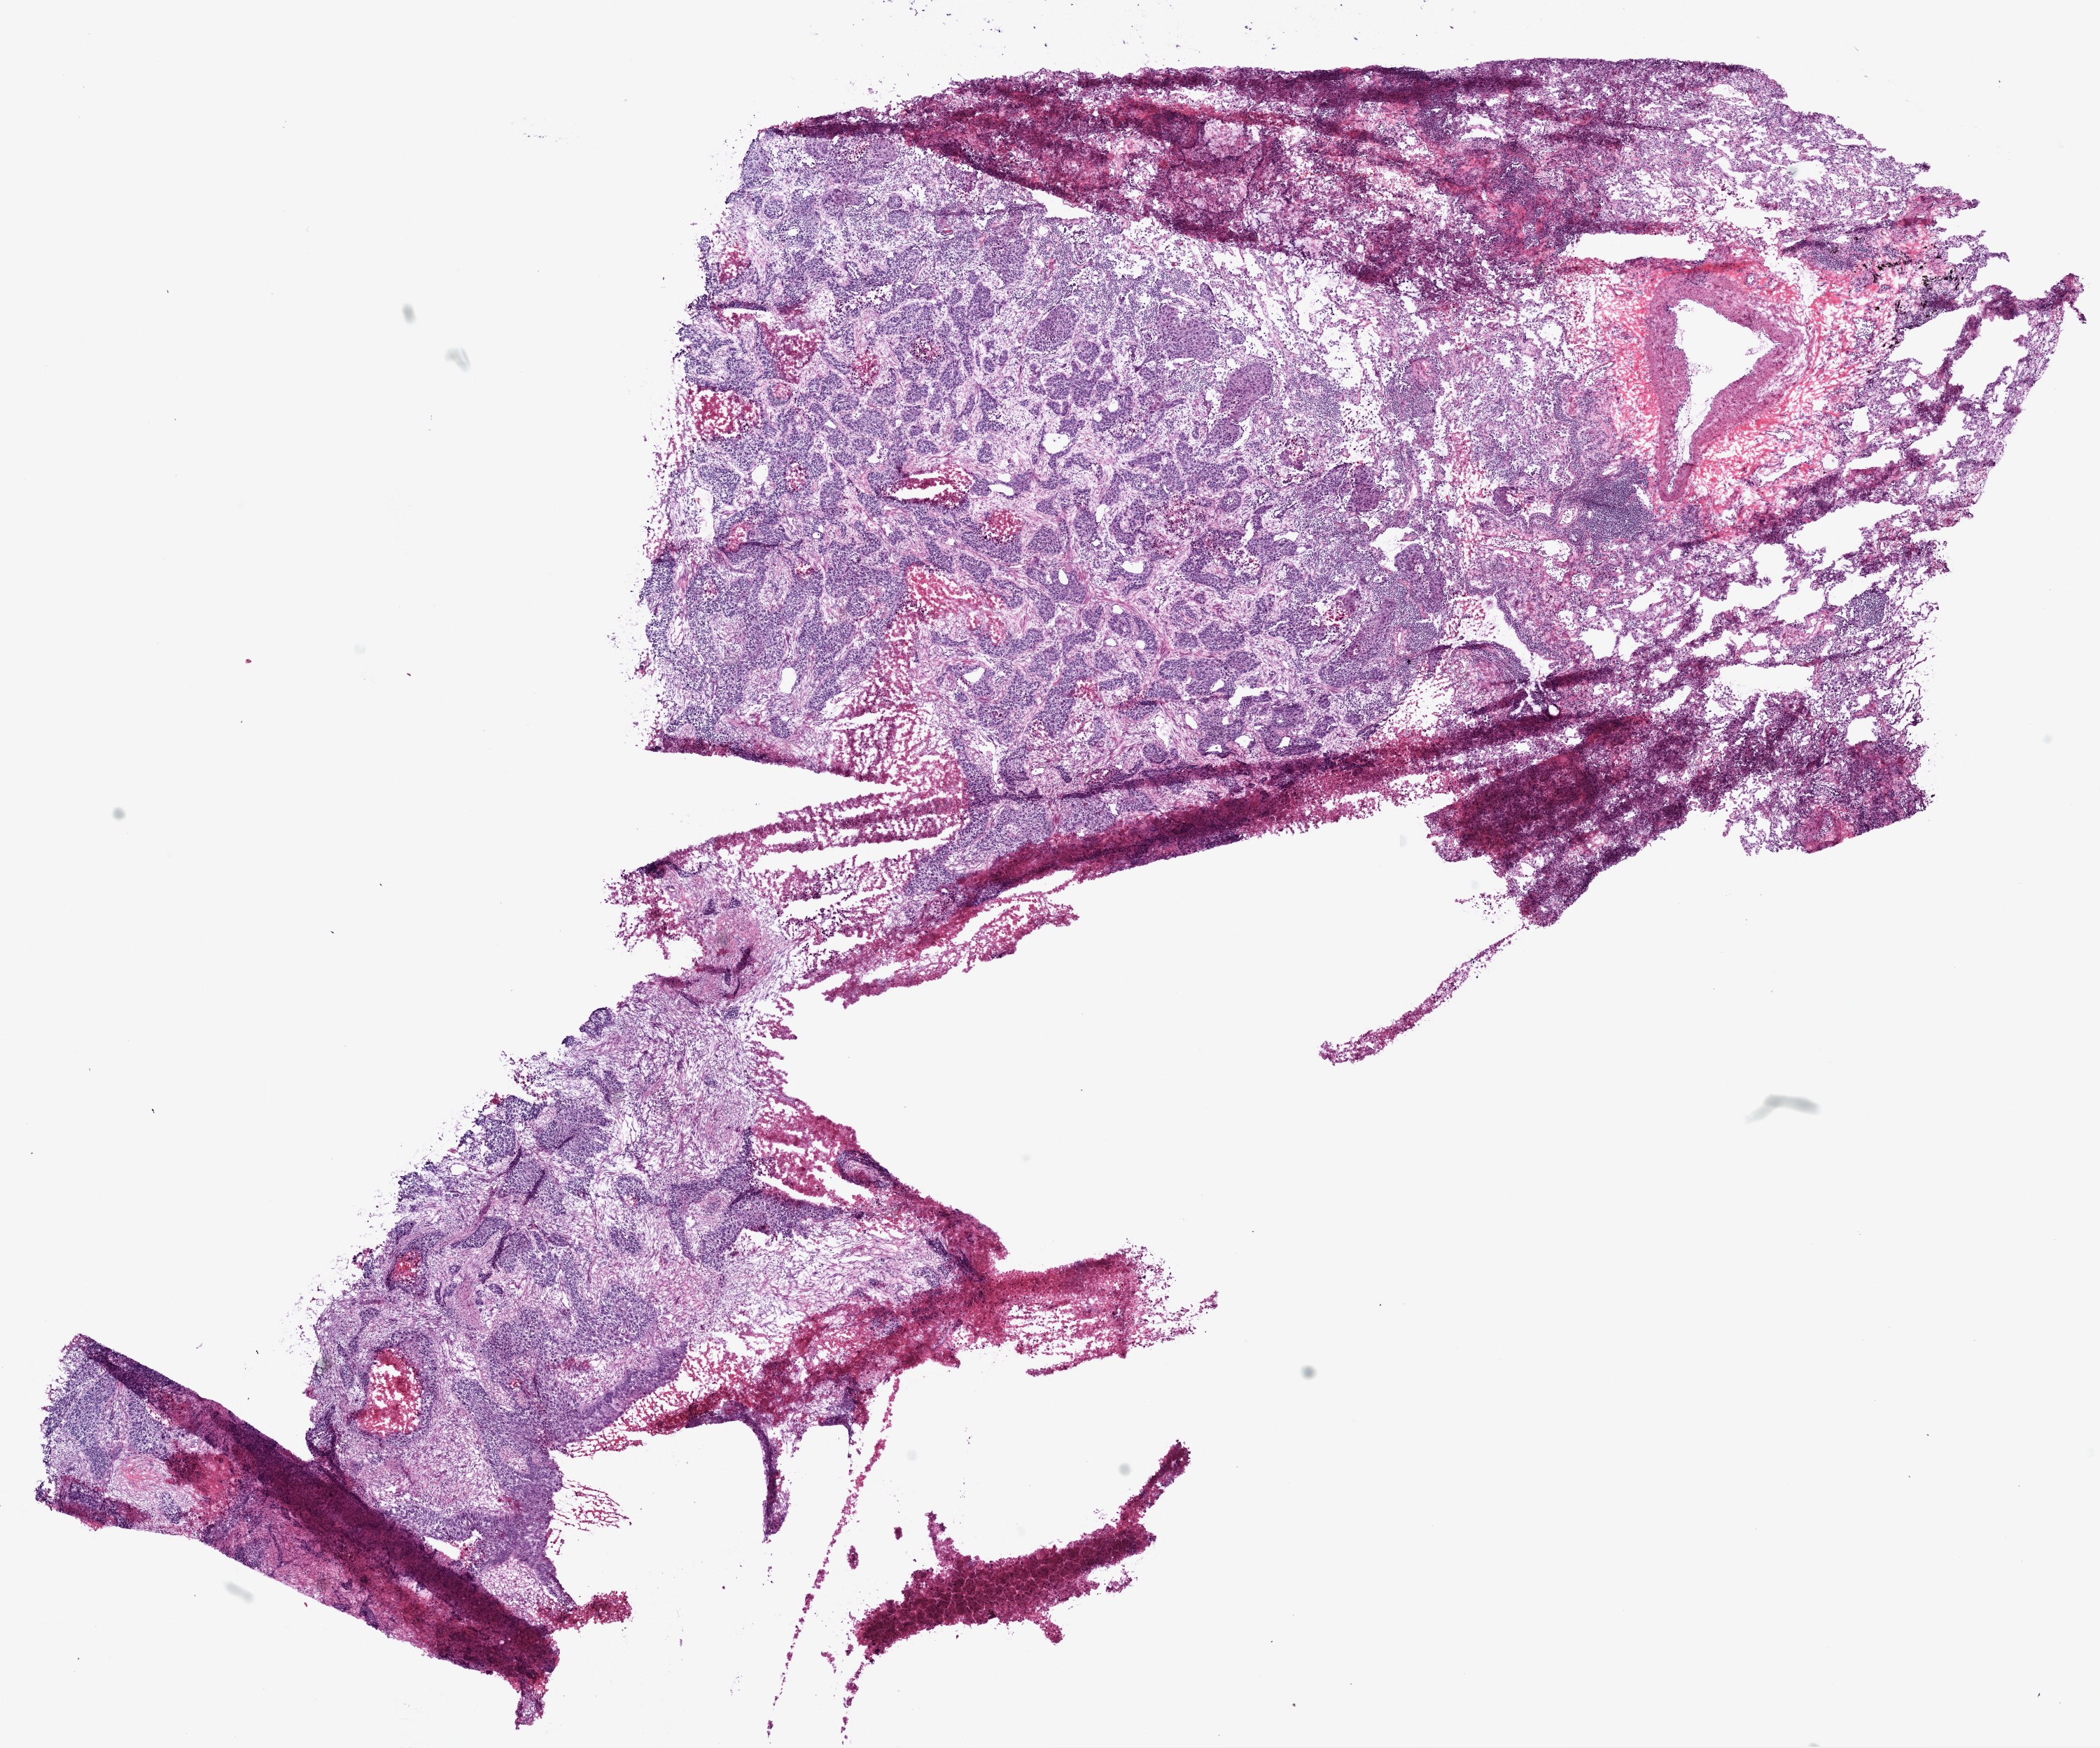
Hematoxylin and eosin (H&E) stained whole-slide image — whole scanned area (about 12.0 x 10.0 mm, acquisition: 20x scan) shown as a low-resolution overview; frozen section; lung, primary tumour sample. Male patient; age at initial diagnosis 70 years. Composition of this section per pathologist review: tumour cells 60%, tumour nuclei 70%, normal cells 15%, stromal cells 15%, necrosis 10%. Infiltration values recorded for this section: lymphocyte infiltration 20%, monocyte infiltration 1%, neutrophil infiltration 0%.
TNM: T4 N0 M0. AJCC pathologic stage: IIIB (5th edition). Diagnosis: Squamous cell carcinoma, NOS (upper lobe, lung).